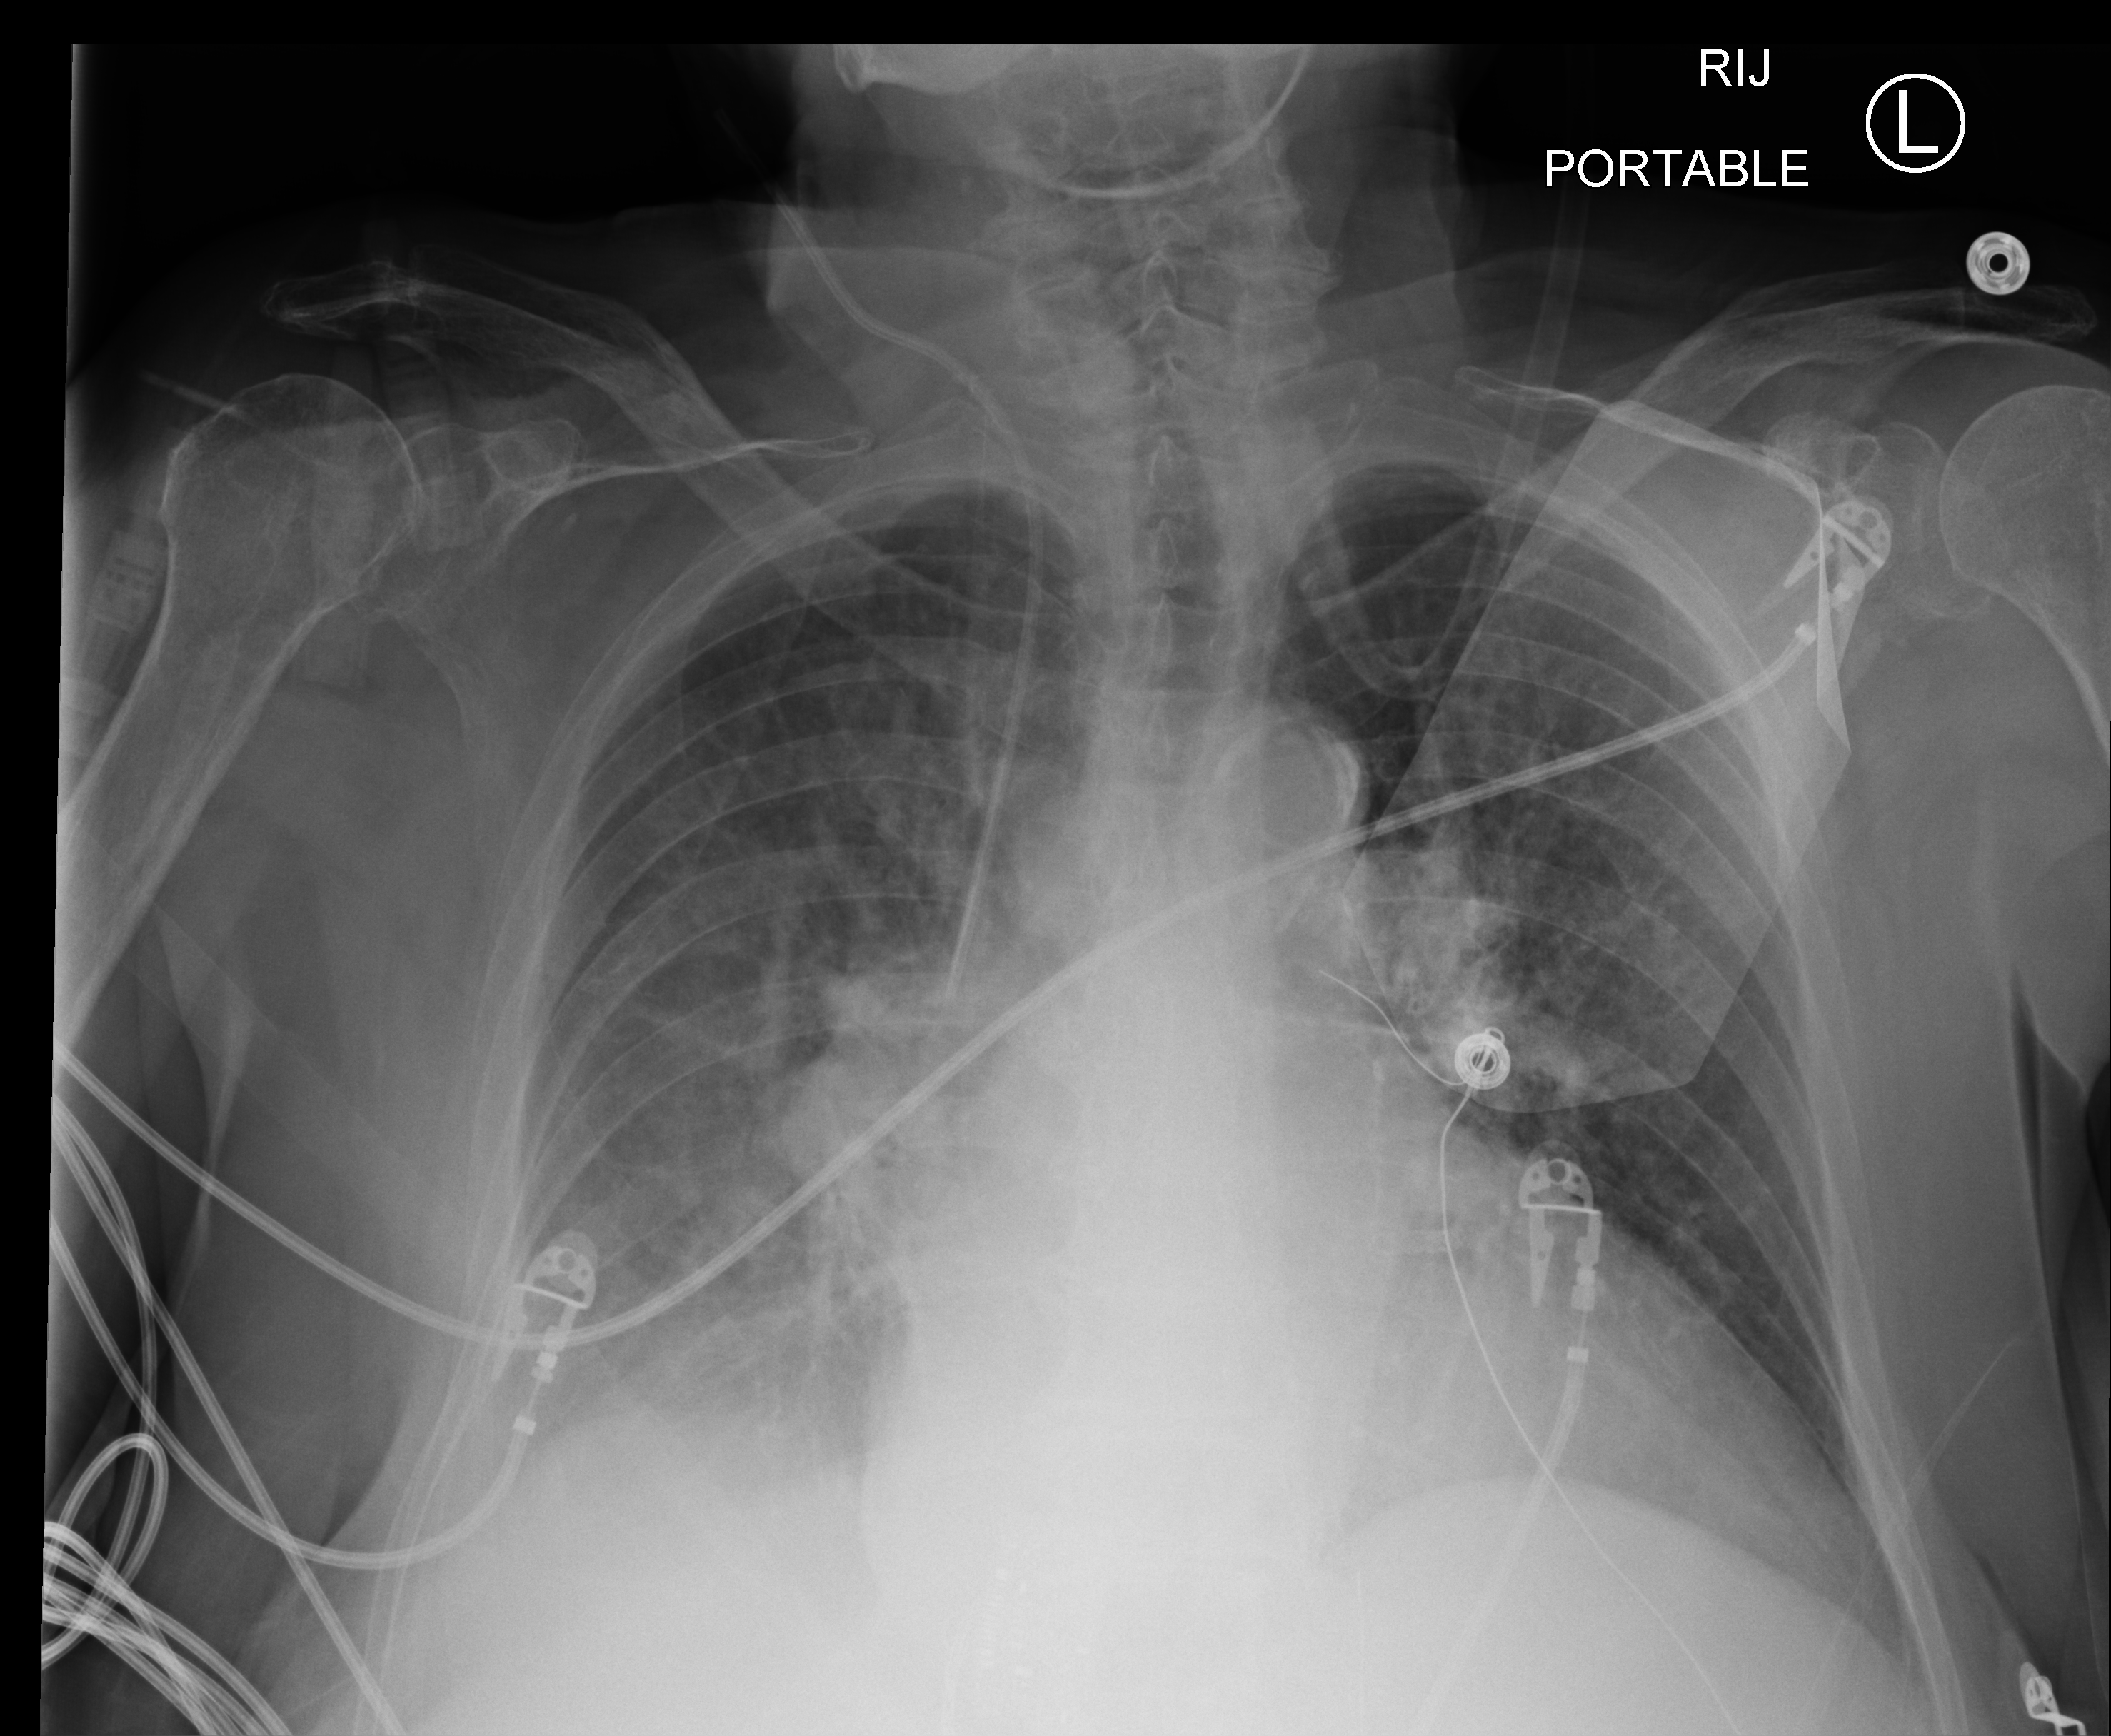
Bedside chest radiograph (computed radiography). Female patient hospitalised with COVID-19, age 75–90 years.
Admission-level facts for this patient (not findings on this image; timing relative to this image not recorded): diabetes (admission record): no.